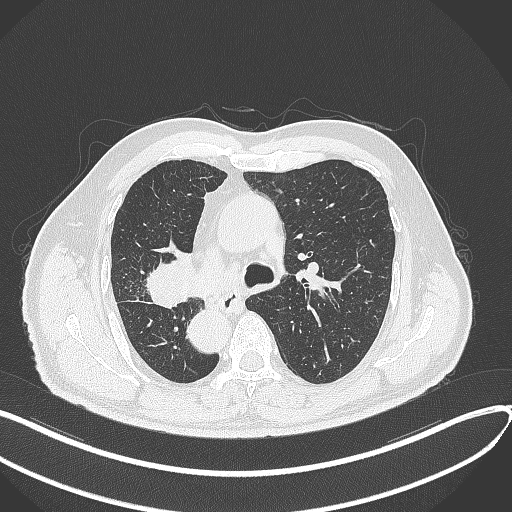
Chest CT, one axial slice; slice 203 of 300 in the series (ordered by position); 120 kVp; lung window (W 1500 / L -600 HU); 1 mm slice thickness; 512 × 512 image matrix. Patient: male, 67 years. Case-level facts recorded for this patient, not image findings: clinical TNM (as recorded): T2a N0 M0.
Outlined on this slice (bounding box drawn by a radiologist):
- lung tumour (recorded histology: squamous cell carcinoma): box from (x=144, y=246) to (x=199, y=309) px